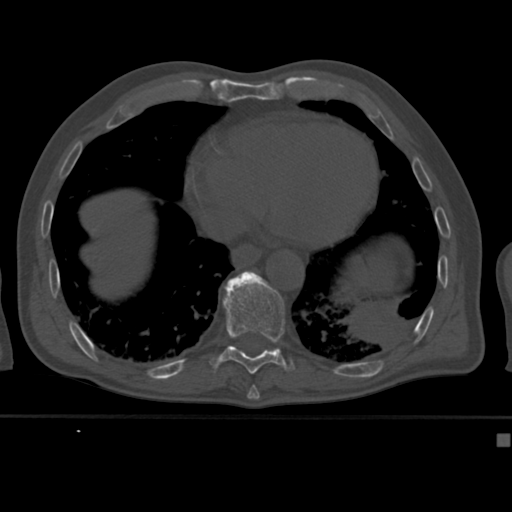
CT including the spine, one axial slice. Position 228 of 430 along the scan axis. 120 kVp. Bone window (W 1800 / L 400 HU). 1.5 mm slice thickness. 512 × 512 image matrix, field of view 337 × 337 mm. Patient: male, 64 years. Case-level facts recorded for this patient, not image findings: primary cancer: uterus; vertebrae with lytic lesions (as recorded): T1, T4, T5, T7, L5.
Annotated regions visible in this slice (semi-automatic segmentation, software-assisted and operator-edited):
- T10 vertebra: bounding box [x1, y1, x2, y2] px = [210, 271, 295, 374]